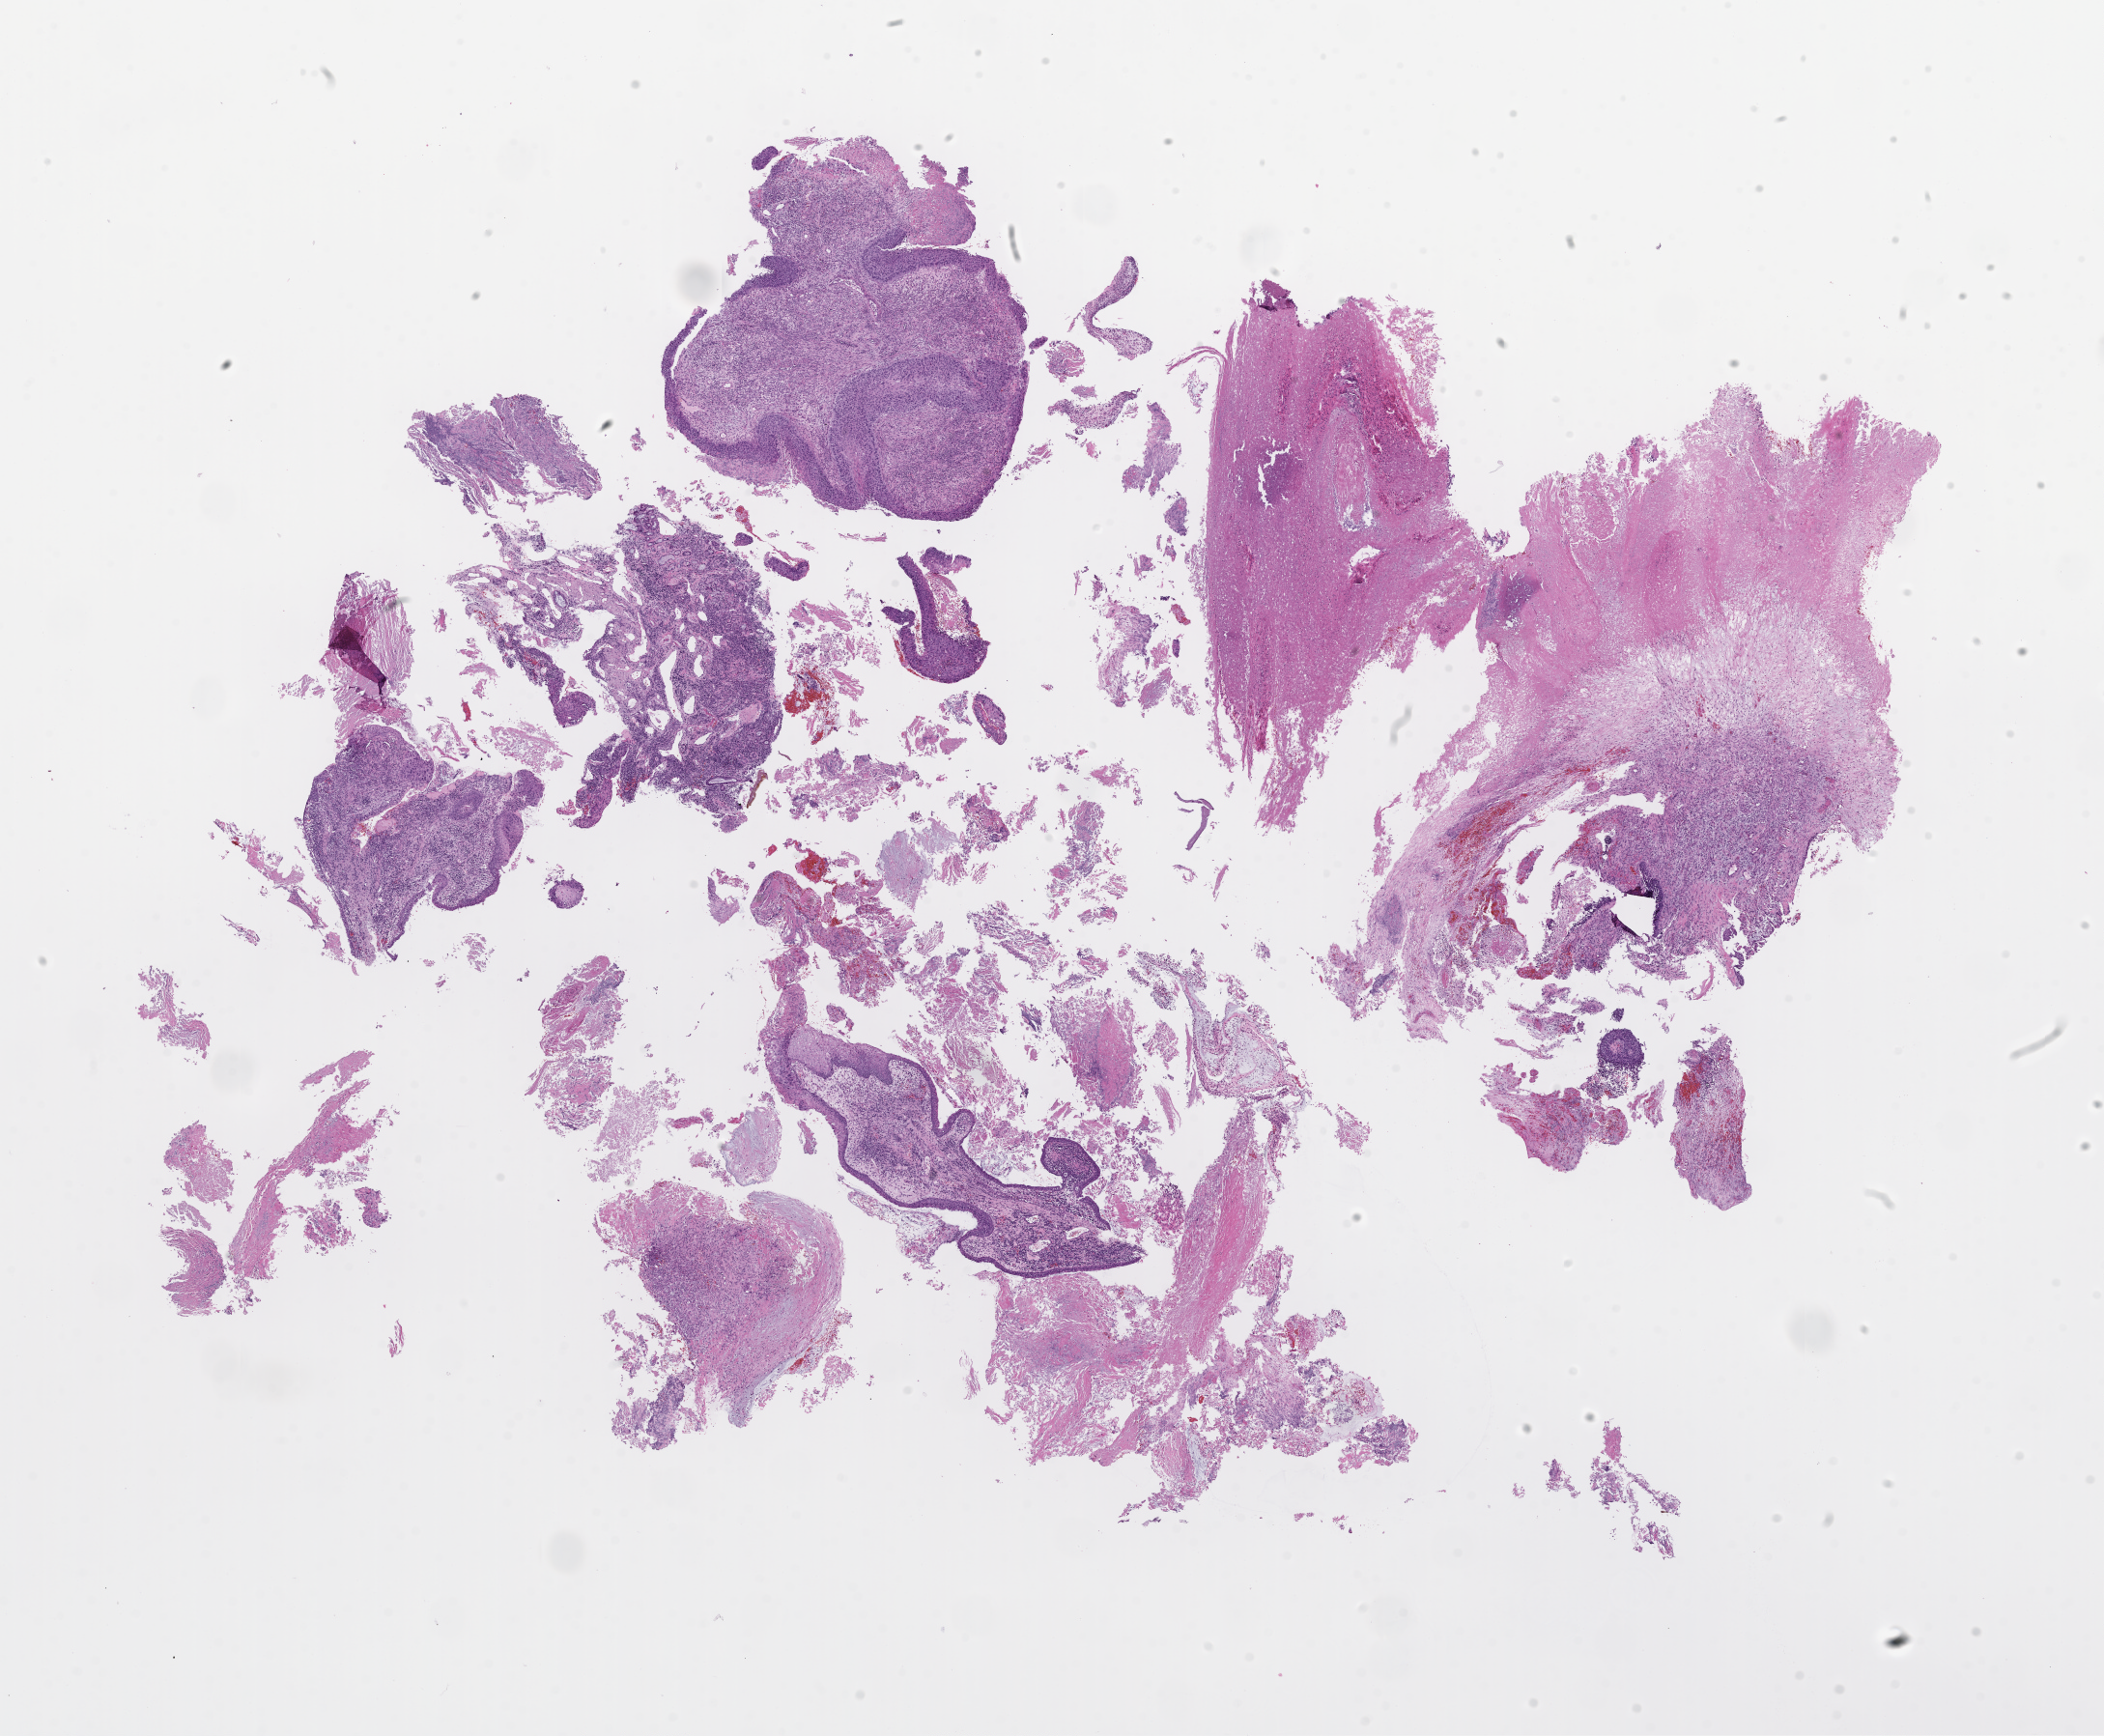
Digitized H&E-stained section, whole scanned area (about 17.6 x 14.5 mm) shown as a low-resolution overview; FFPE section; tissue site: lung; archival tissue. Male patient.
This section: primary tumor. Diagnosis: Non-Small Cell Lung Carcinoma.